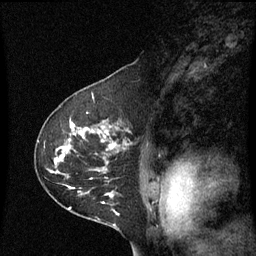
Breast MRI (dynamic contrast-enhanced), one sagittal slice; slice 42 of 60 in the series (ordered by position); dynamic contrast-enhanced series, image 2 of 3 at this slice position (ordered by acquisition); 1.5 T; TE 4.2 ms, TR 8.9 ms; 2 mm slice thickness; 256 × 256 image matrix. Female patient, age 53 years. Case-level facts recorded for this patient, not image findings: setting: breast cancer imaged before/during neoadjuvant chemotherapy; receptor status: HR-positive, HER2-negative.
Outlined on this slice (semi-automatic segmentation, software-assisted and operator-edited):
- analysis volume of interest (the breast-tissue region the enhancement analysis was run in; not a lesion): bounding box (x1, y1, x2, y2) in pixels: (36, 100, 145, 221)
- tumour enhancement mask (voxels above the 70 % enhancement threshold inside the analysis volume of interest): (54, 124, 119, 215)